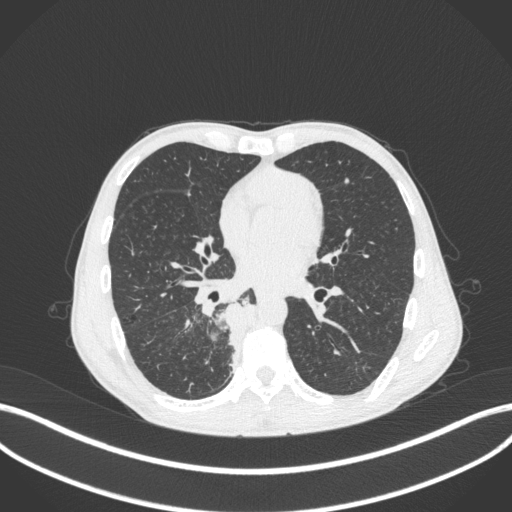
Chest CT, one axial slice; slice 178 of 371 in the series (ordered by position); reconstruction kernel B31f; 120 kVp; lung window (W 1500 / L -600 HU); 512 × 512 image matrix, field of view 400 × 400 mm. Patient: male, 58 years. From the clinical record (not read from this slice): clinical TNM (as recorded): T3 N1 M1.
Structures marked on this image (bounding box drawn by a radiologist):
- lung tumour (recorded histology: squamous cell carcinoma): bounding box <208,300,263,375> (left, top, right, bottom; pixels)